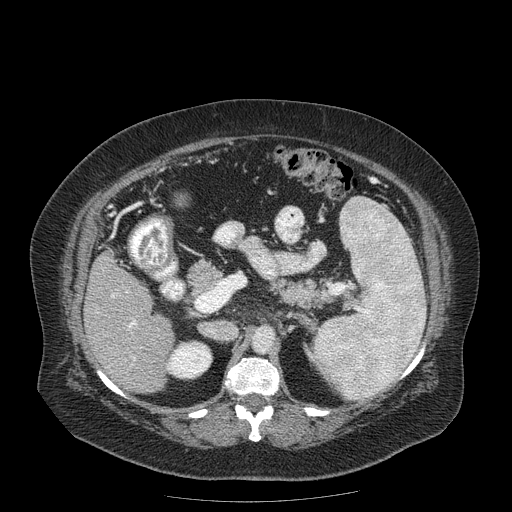
Contrast-enhanced abdominal CT (liver protocol), one axial slice; position 85 of 204 along the scan axis; reconstruction kernel STANDARD; soft-tissue window (W 400 / L 40 HU); 512 × 512 image matrix, field of view 440 × 440 mm. From the clinical record (not read from this slice): diagnosis: hepatocellular carcinoma (patient treated with transarterial chemoembolisation; whether this scan precedes or follows treatment is not stated here); TNM stage (as recorded): Stage-IIIB; Child-Pugh class: A; tumour differentiation: well differentiated; tumour nodularity: uninodular.
Structures marked on this image (semi-automatically segmented with operator editing):
- liver parenchyma outside the tumour (the mass and vessels are separate outlines, so this box may not span the whole liver): bounding box <84,252,174,392> (left, top, right, bottom; pixels)
- liver vessels: <111,294,136,359>